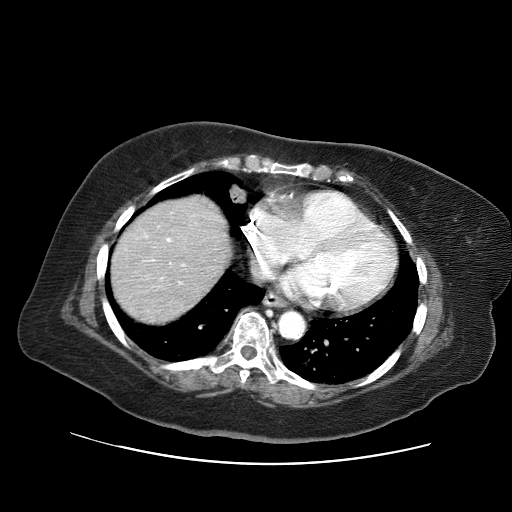
Contrast-enhanced abdominal CT (liver protocol), one axial slice; slice 60 of 71 in the series (ordered by position); reconstruction kernel STANDARD; soft-tissue window (W 400 / L 40 HU); 2.5 mm slice thickness; 512 × 512 image matrix. From the clinical record (not read from this slice): diagnosis: hepatocellular carcinoma (patient treated with transarterial chemoembolisation; whether this scan precedes or follows treatment is not stated here); TNM stage (as recorded): Stage-II; Child-Pugh class: A; tumour differentiation: poorly differentiated; tumour nodularity: multinodular.
Structures marked on this image (semi-automatic segmentation, software-assisted and operator-edited):
- abdominal aorta: bounding box <278,312,303,338> (left, top, right, bottom; pixels)
- liver parenchyma outside the tumour (the mass and vessels are separate outlines, so this box may not span the whole liver): <110,196,230,322>
- liver vessels: <144,234,186,285>